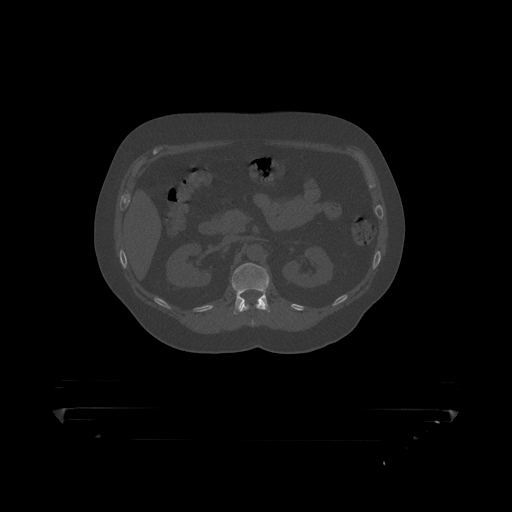
CT including the spine, one axial slice. Slice 155 of 390 in the series (ordered by position). 120 kVp. Bone window (W 1800 / L 400 HU). 512 × 512 image matrix. Male patient, age 60 years. Case-level facts recorded for this patient, not image findings: primary cancer: prostate.
Structures marked on this image (semi-automatically segmented with operator editing):
- L1 vertebra: box from (x=232, y=263) to (x=271, y=315) px
- T12 vertebra: (x=237, y=300)–(x=269, y=314)